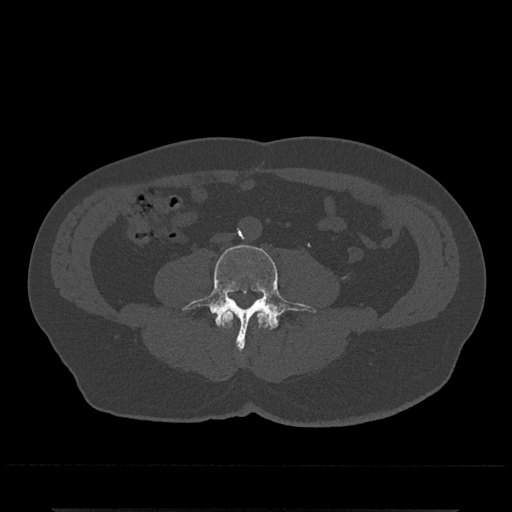
CT including the spine, one axial slice. Slice 162 of 797 in the series (ordered by position). Reconstruction kernel Br40s/3. 120 kVp. Bone window (W 1800 / L 400 HU). 0.5 mm slice thickness. 512 × 512 image matrix, field of view 393 × 393 mm. Male patient, age 67 years. Case-level facts recorded for this patient, not image findings: primary cancer: prostate.
Annotated regions visible in this slice (semi-automatically segmented with operator editing):
- L3 vertebra: box from (x=220, y=310) to (x=270, y=328) px
- L4 vertebra: (x=182, y=244)–(x=316, y=350)